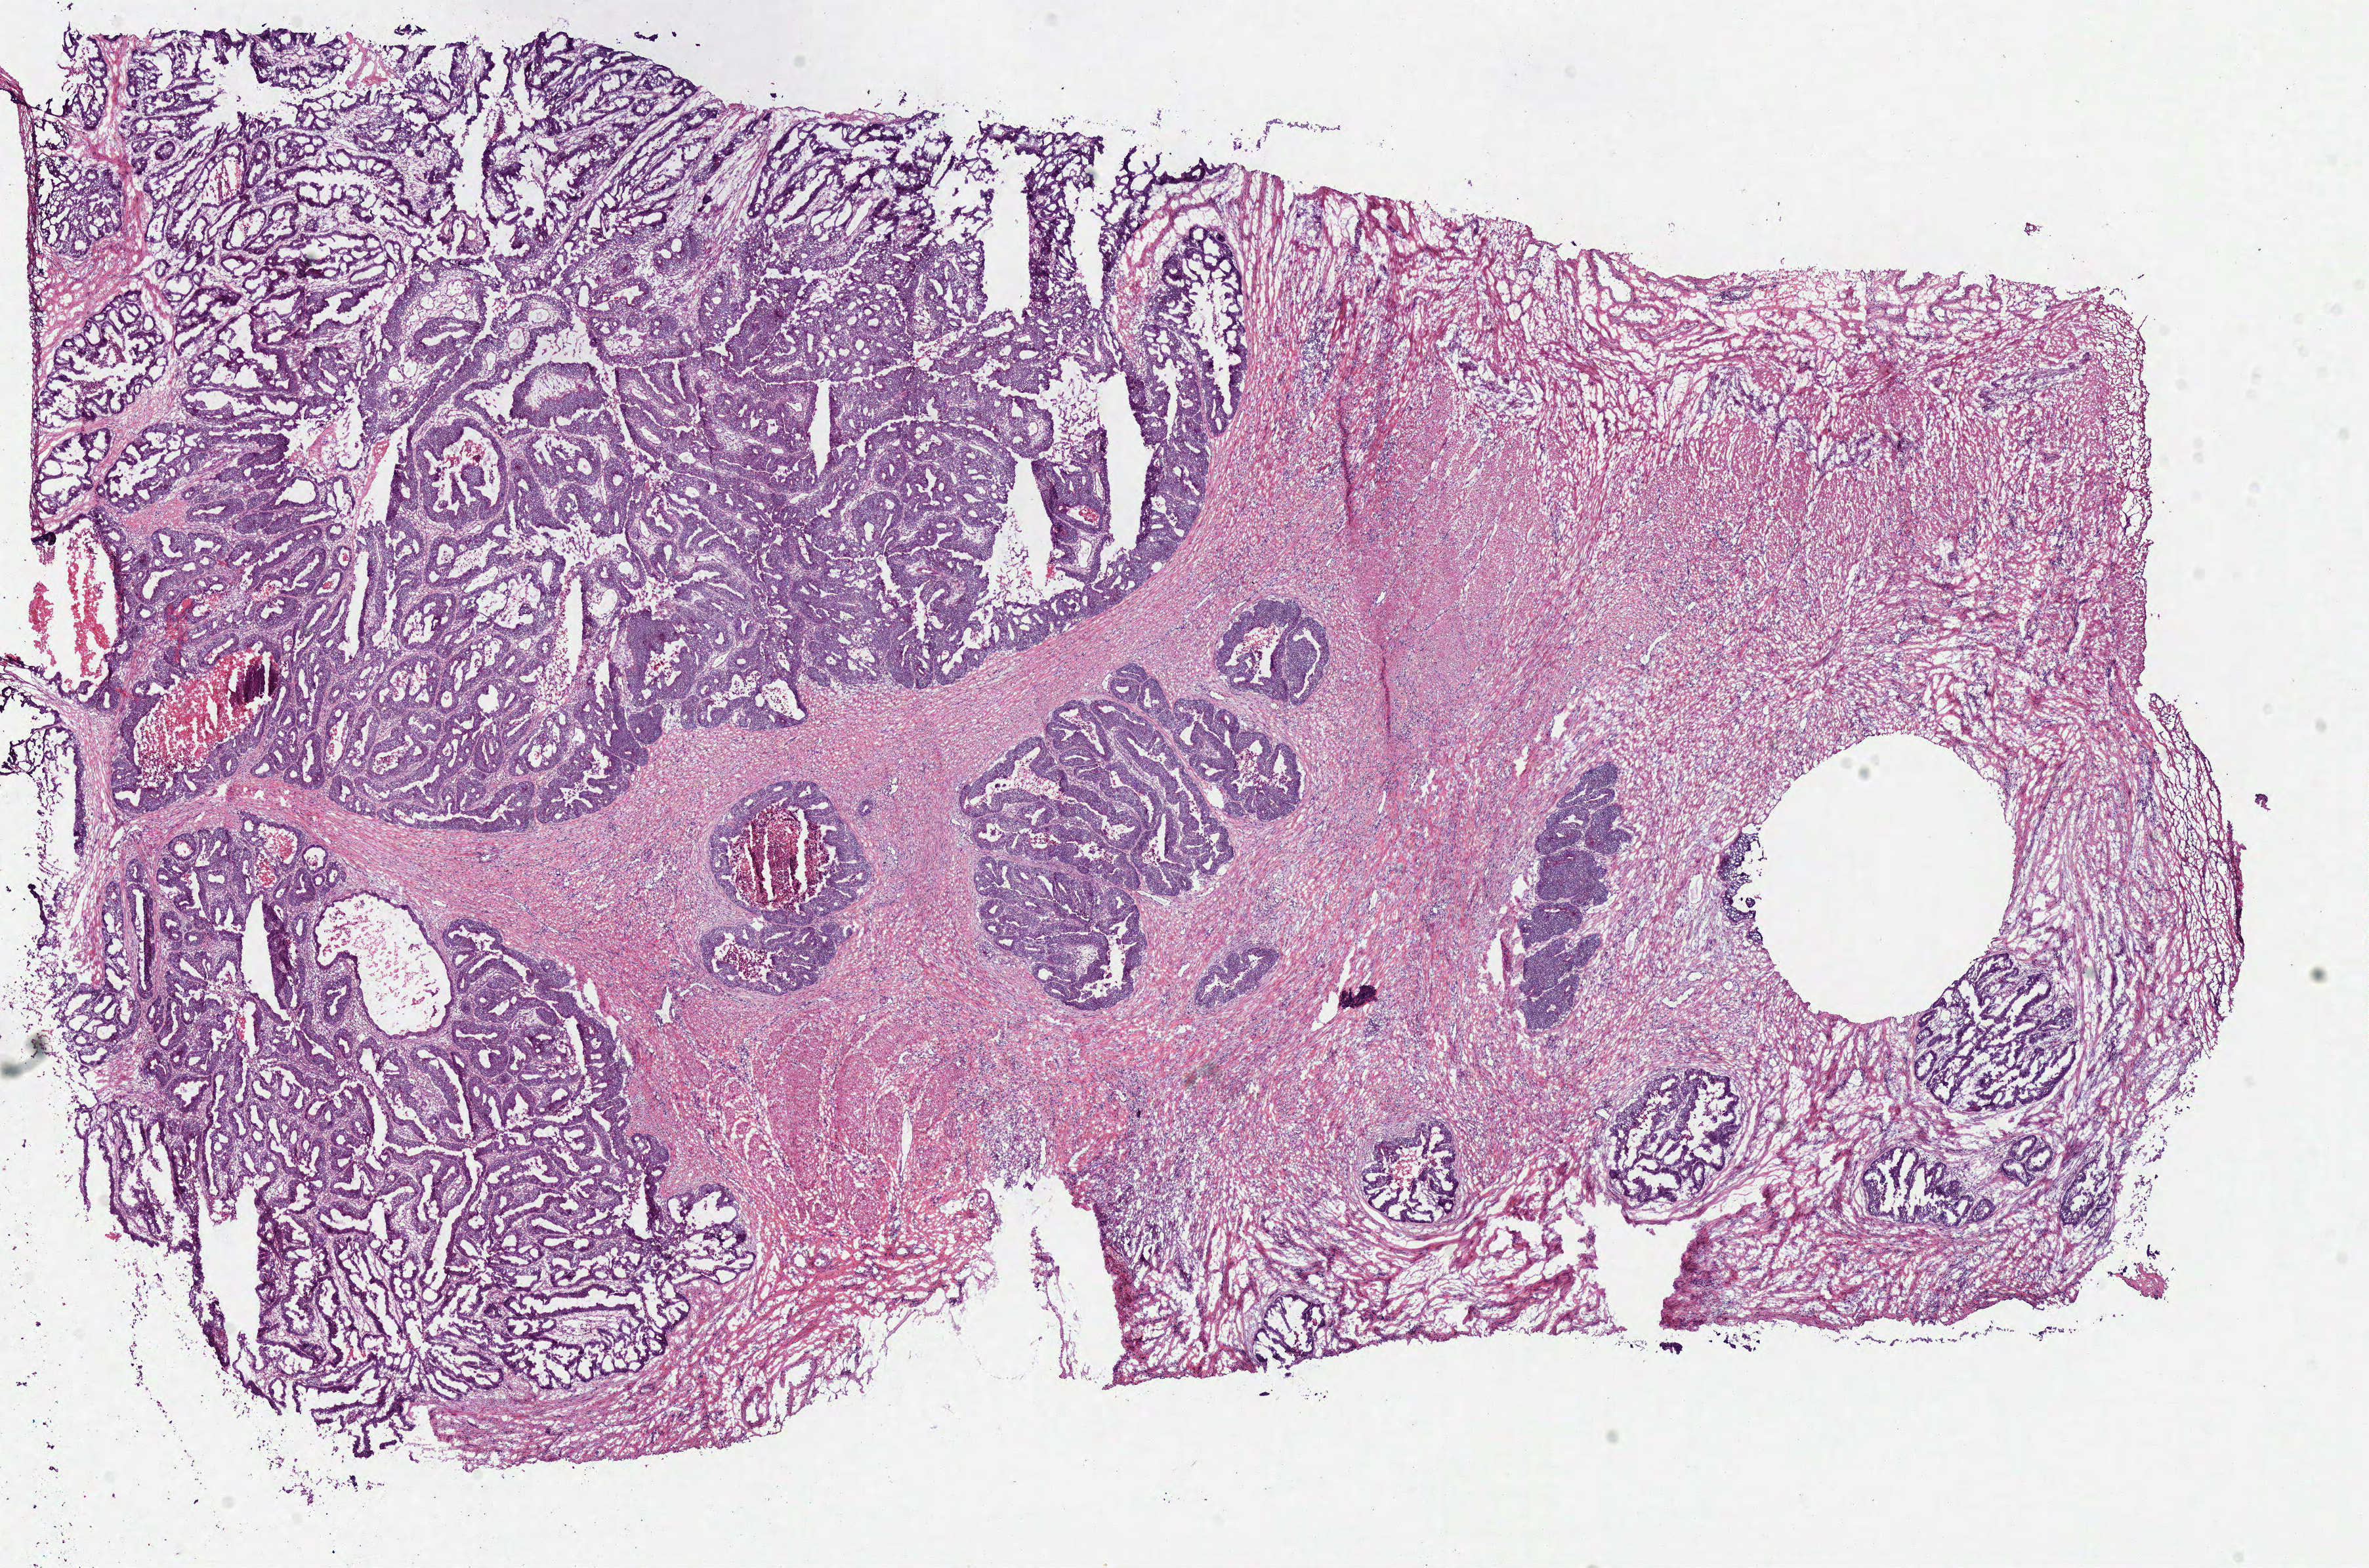
H&E whole-slide image, shown as a low-resolution overview of the whole scanned area (about 14.2 x 9.4 mm); frozen section; colon, primary tumour sample. Patient: male, age at initial diagnosis 65 years. Slide review estimates, as recorded: tumour cells 67%, tumour nuclei 80%, normal cells 0%, stromal cells 25%, necrosis 8%.
Pathologic diagnosis: Papillary adenocarcinoma, NOS. AJCC pathologic stage: IIA.